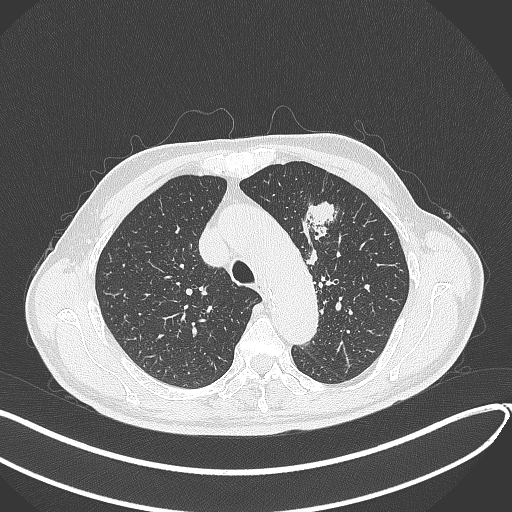
Chest CT, one axial slice. Slice 310 of 459 in the series (ordered by position). Reconstruction kernel B70f. 120 kVp. Lung window (W 1500 / L -600 HU). 512 × 512 image matrix, field of view 400 × 400 mm. Male patient, age 74 years. Case-level facts recorded for this patient, not image findings: clinical TNM (as recorded): T2b N0 M1c.
Annotated regions visible in this slice (bounding box drawn by a radiologist):
- lung tumour (recorded histology: adenocarcinoma): bounding box <296,194,340,242> (left, top, right, bottom; pixels)